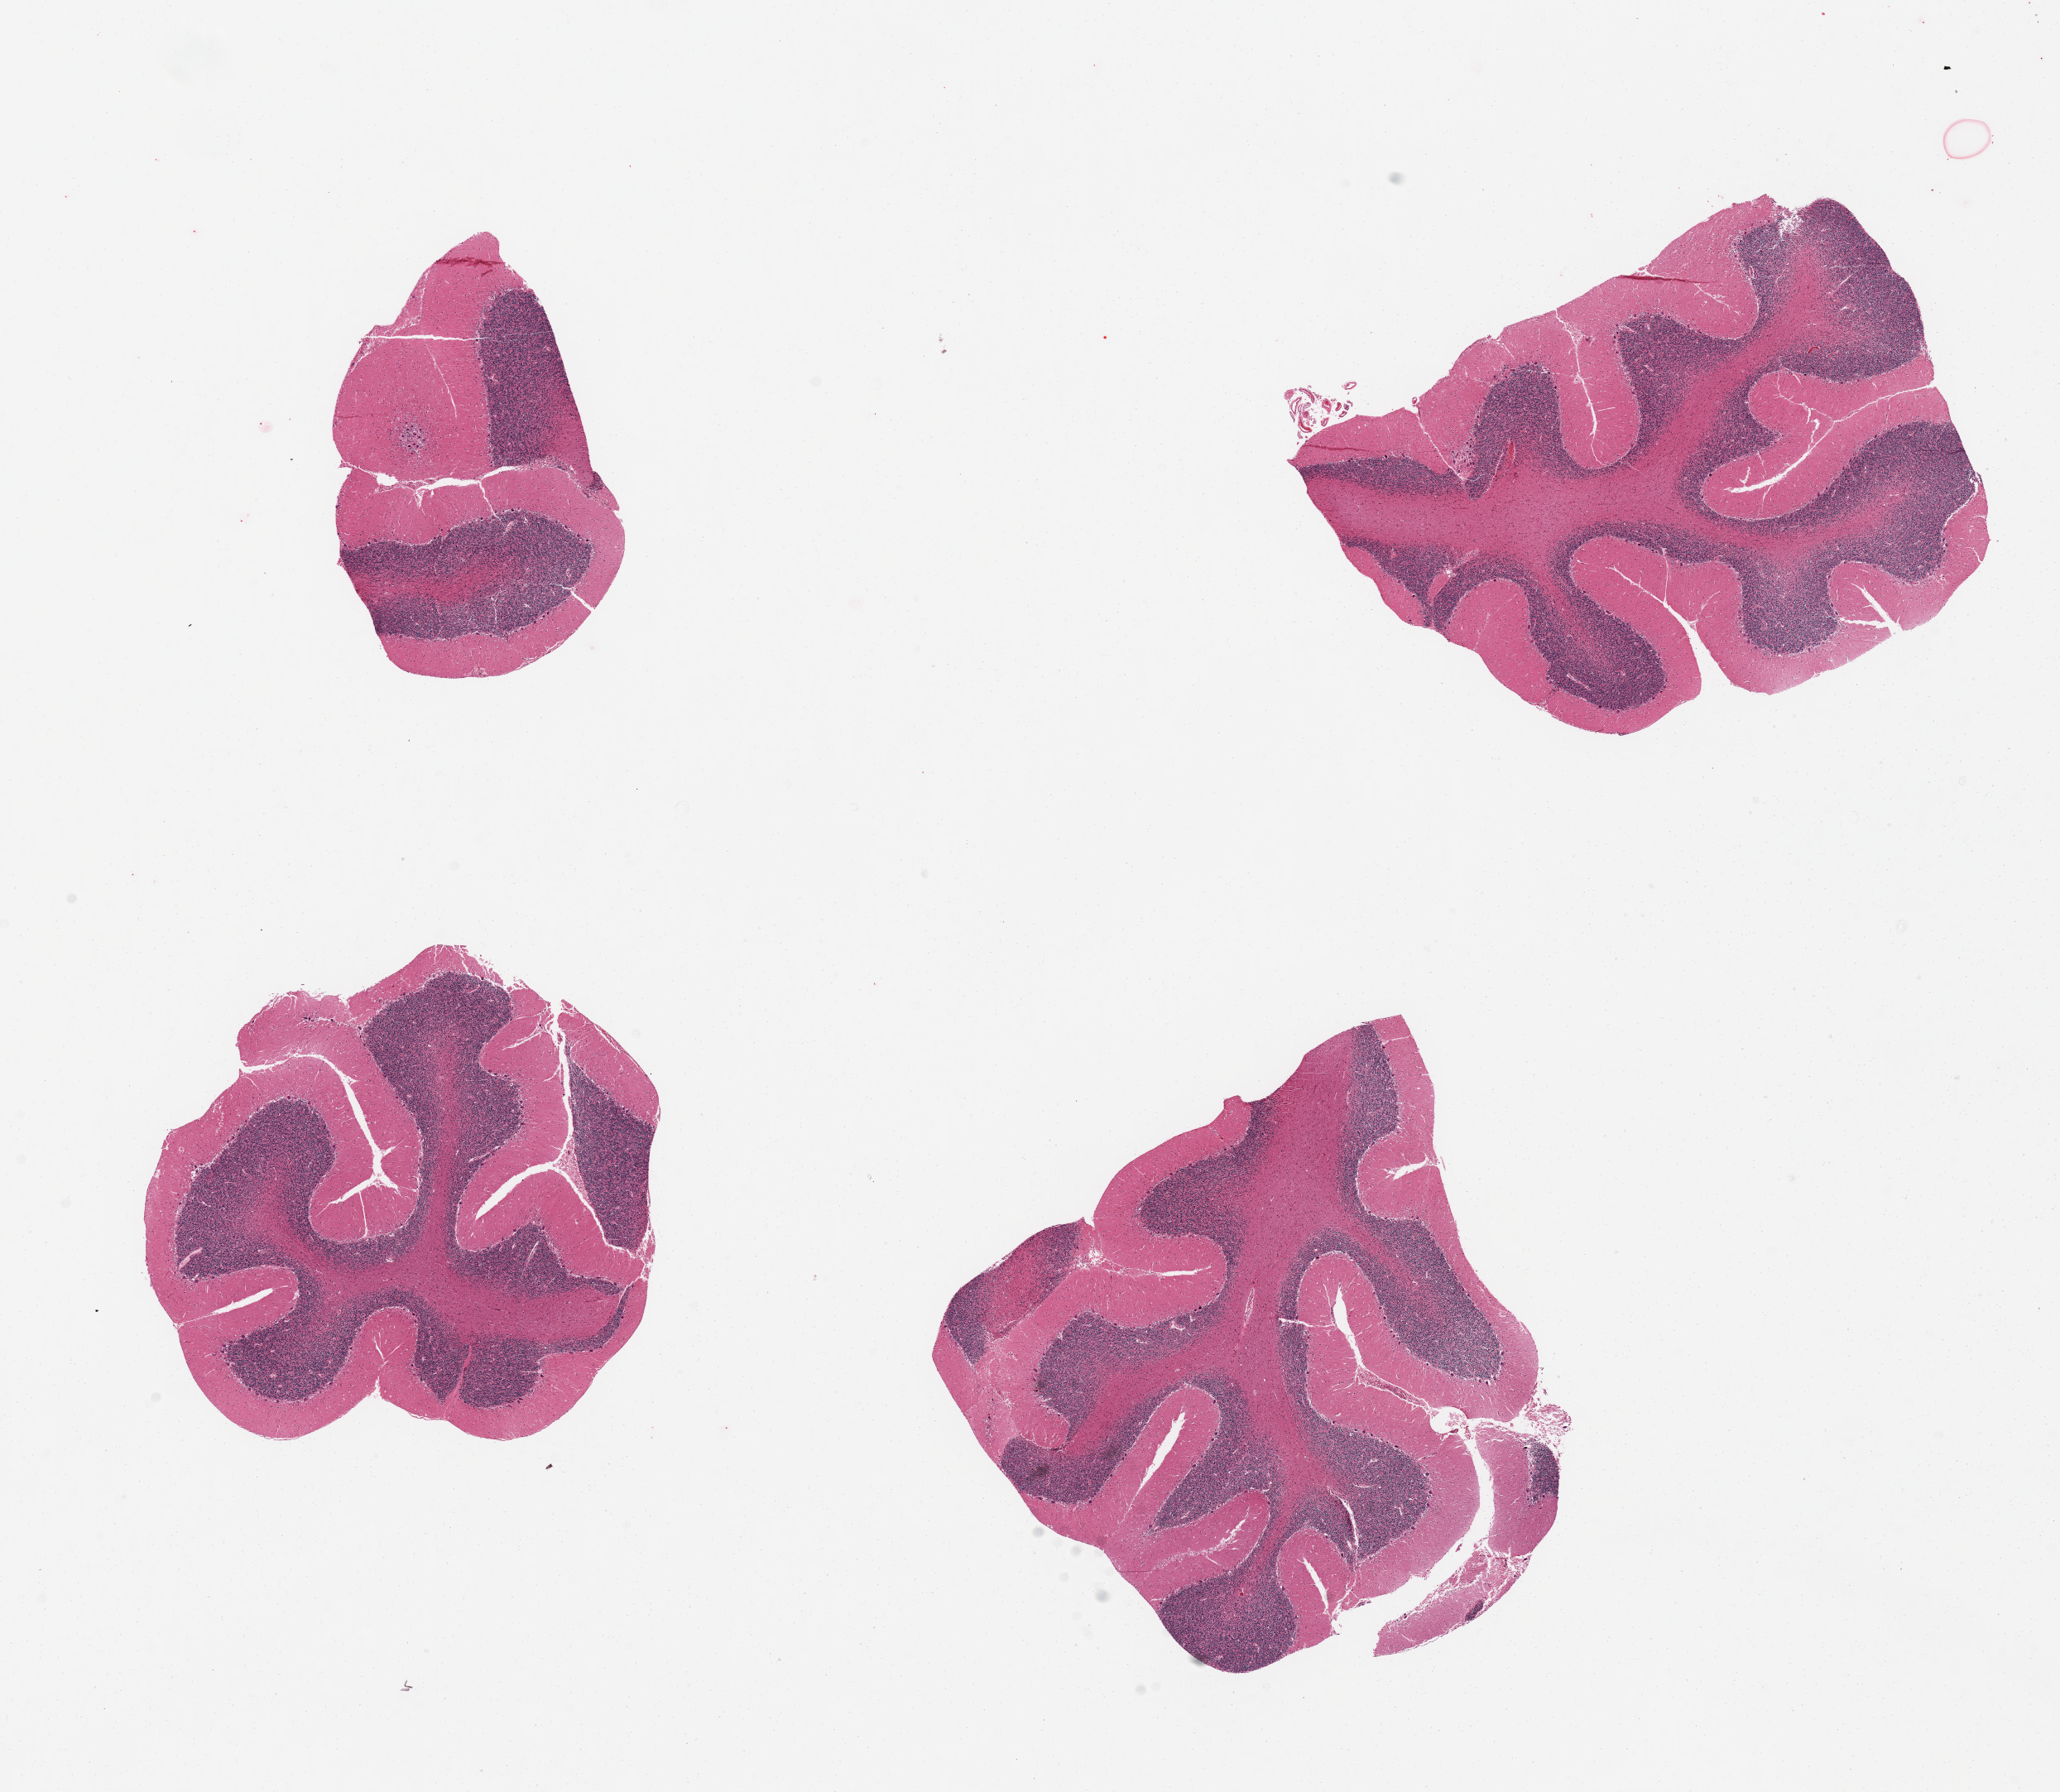
H&E whole-slide image, brightfield, a low-resolution overview of the entire scanned area, about 19.7 x 17.1 mm (from a 20x scan). PAXgene-fixed paraffin-embedded (PFPE) section. Section of cerebellum (target tissue). Tissue donor sample. Male donor.
Review note (as recorded): 4 pieces.